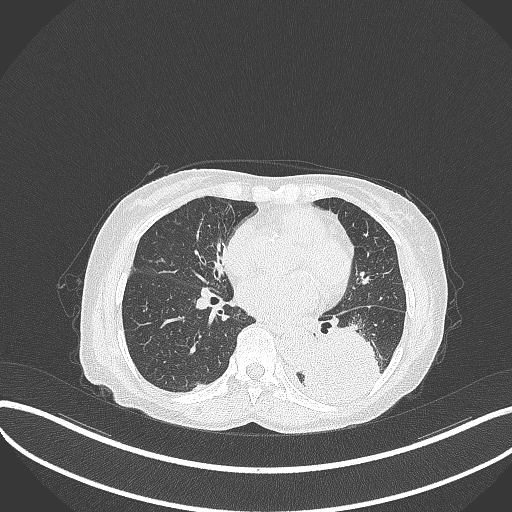
Chest CT, one axial slice; 120 kVp; lung window (W 1500 / L -600 HU); 1 mm slice thickness; 512 × 512 image matrix, field of view 400 × 400 mm. Patient: female, 78 years. Case-level facts recorded for this patient, not image findings: clinical TNM (as recorded): T3 N0 M1.
Outlined on this slice (rectangle marked by the reading radiologist):
- lung tumour (recorded histology: squamous cell carcinoma): bounding box (x1, y1, x2, y2) in pixels: (303, 323, 387, 407)